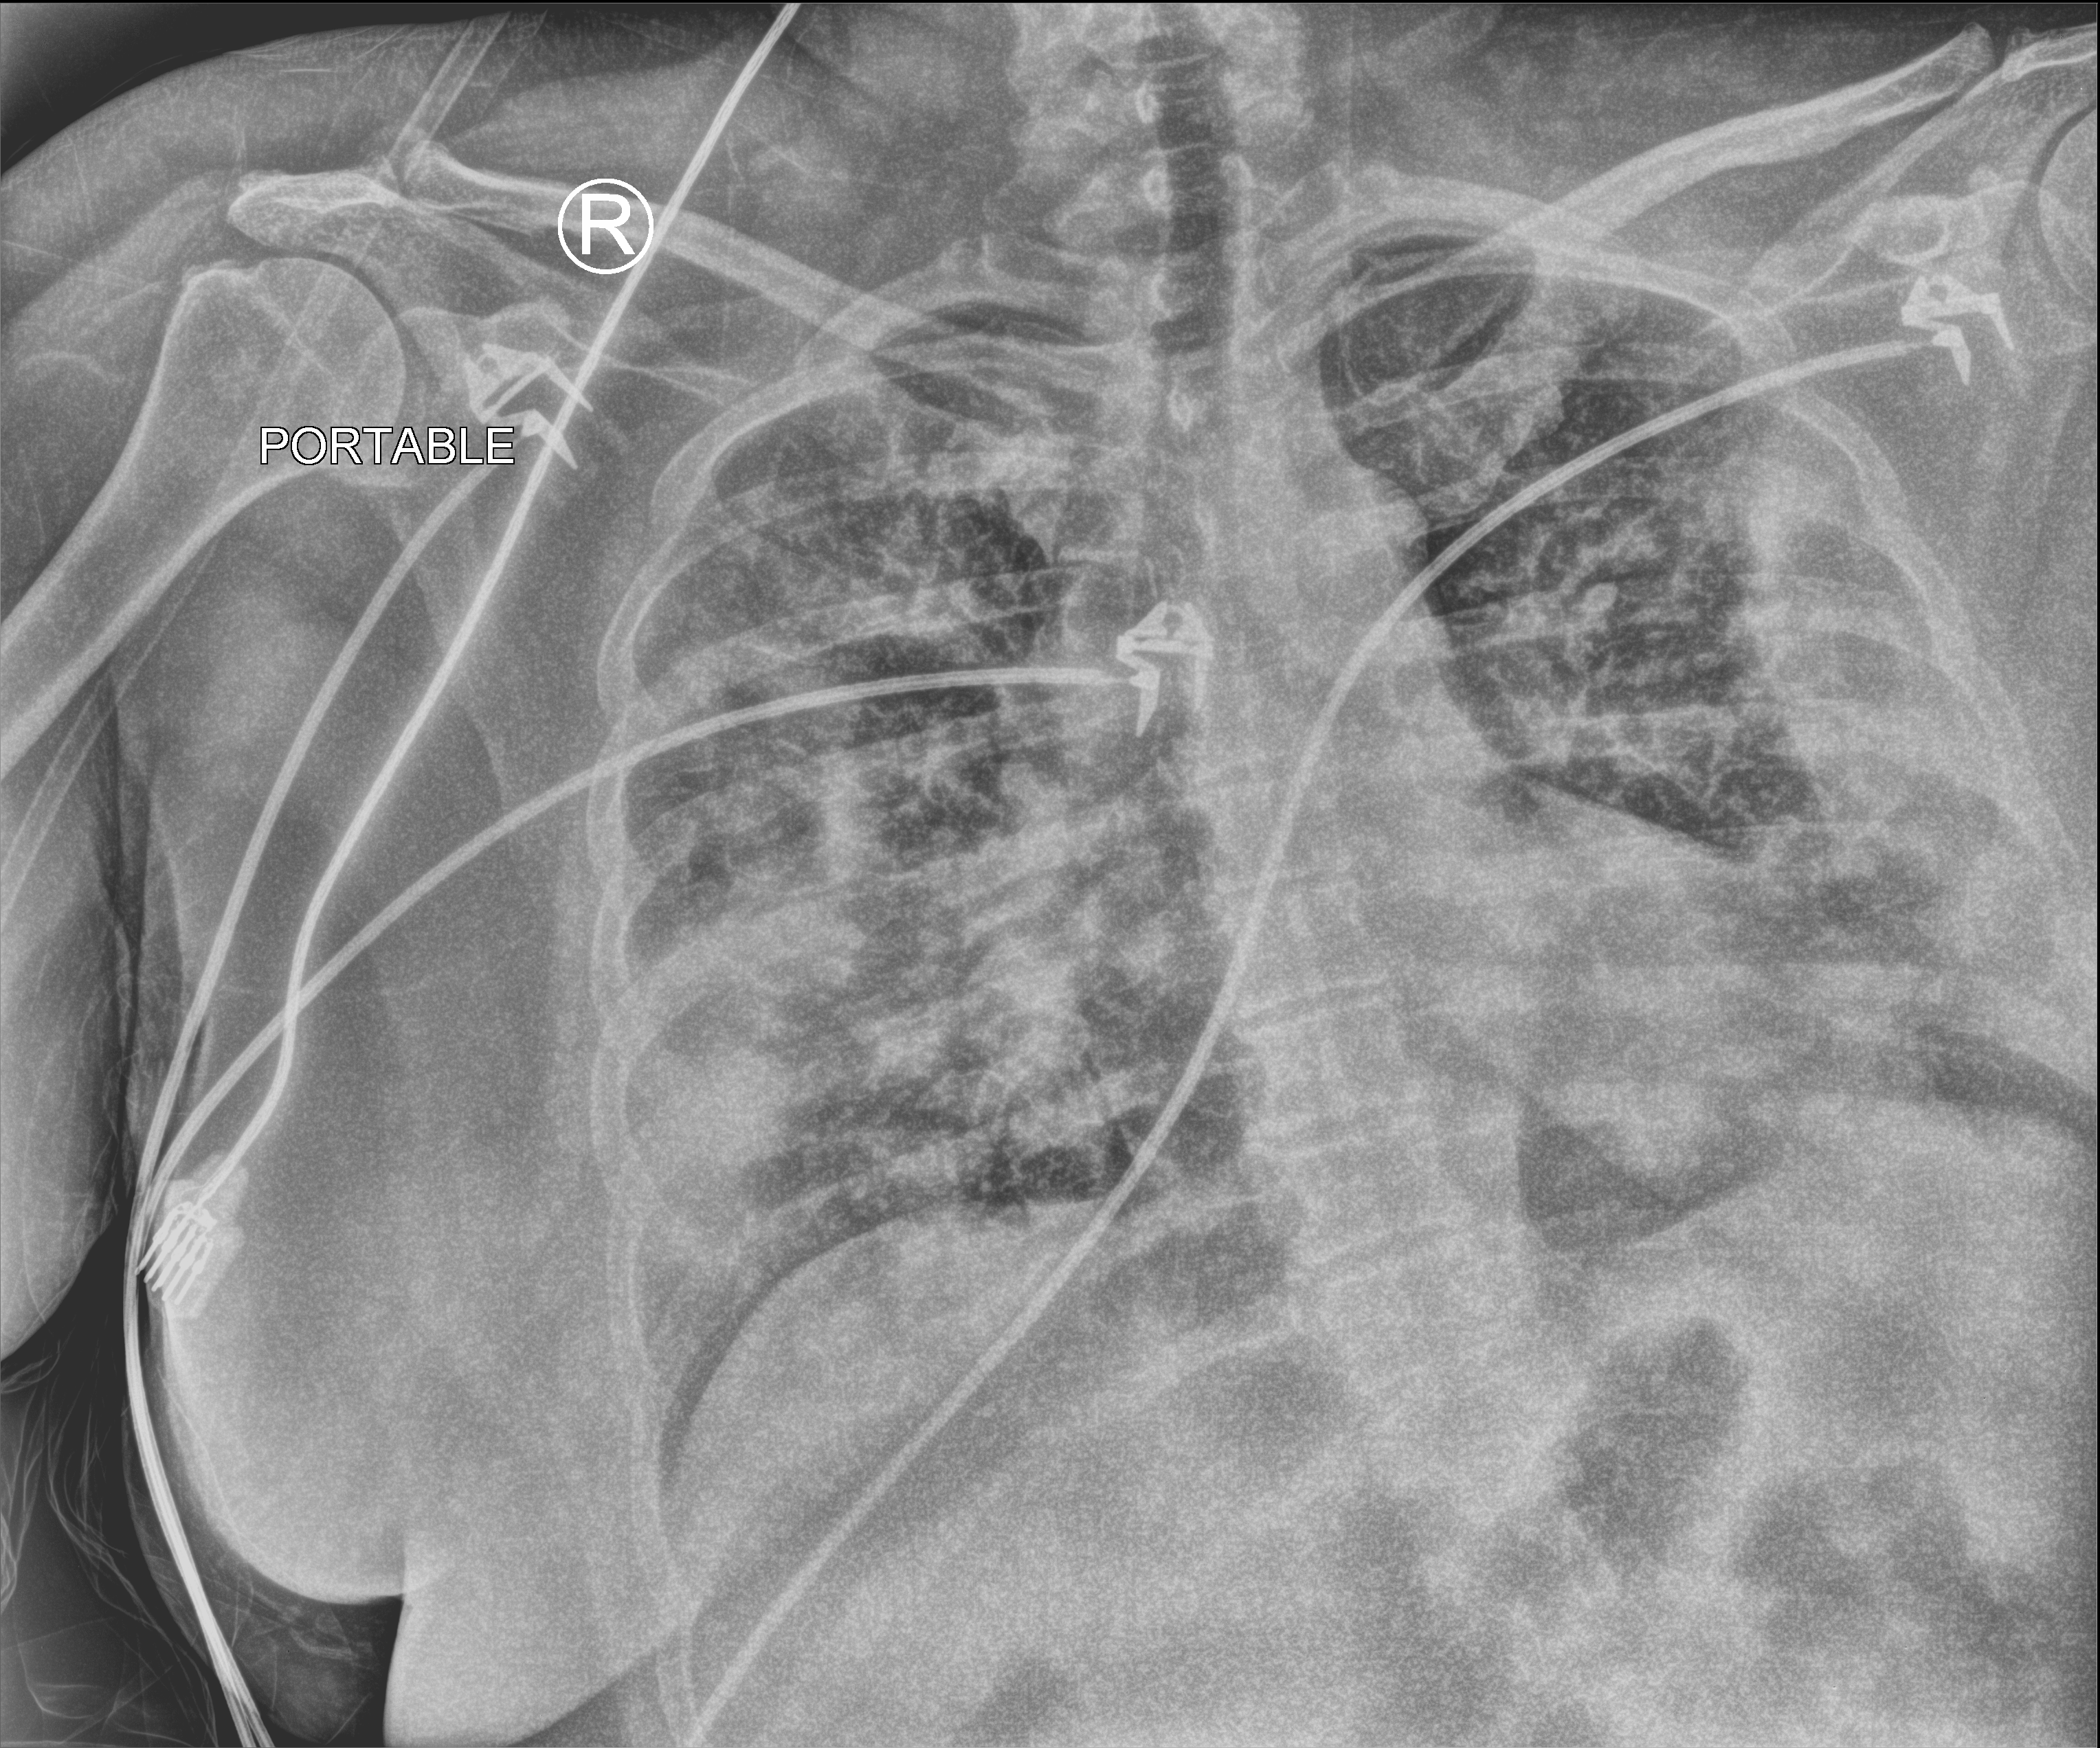
Chest X-ray (portable); anteroposterior (AP) projection. Female patient hospitalised with COVID-19, age 18–59 years.
From the hospital-stay record, not from the radiograph (when in the stay this image was taken is not recorded): chronic kidney disease (admission record): no; admitted to intensive care during this hospital stay: no; COPD (admission record): no.